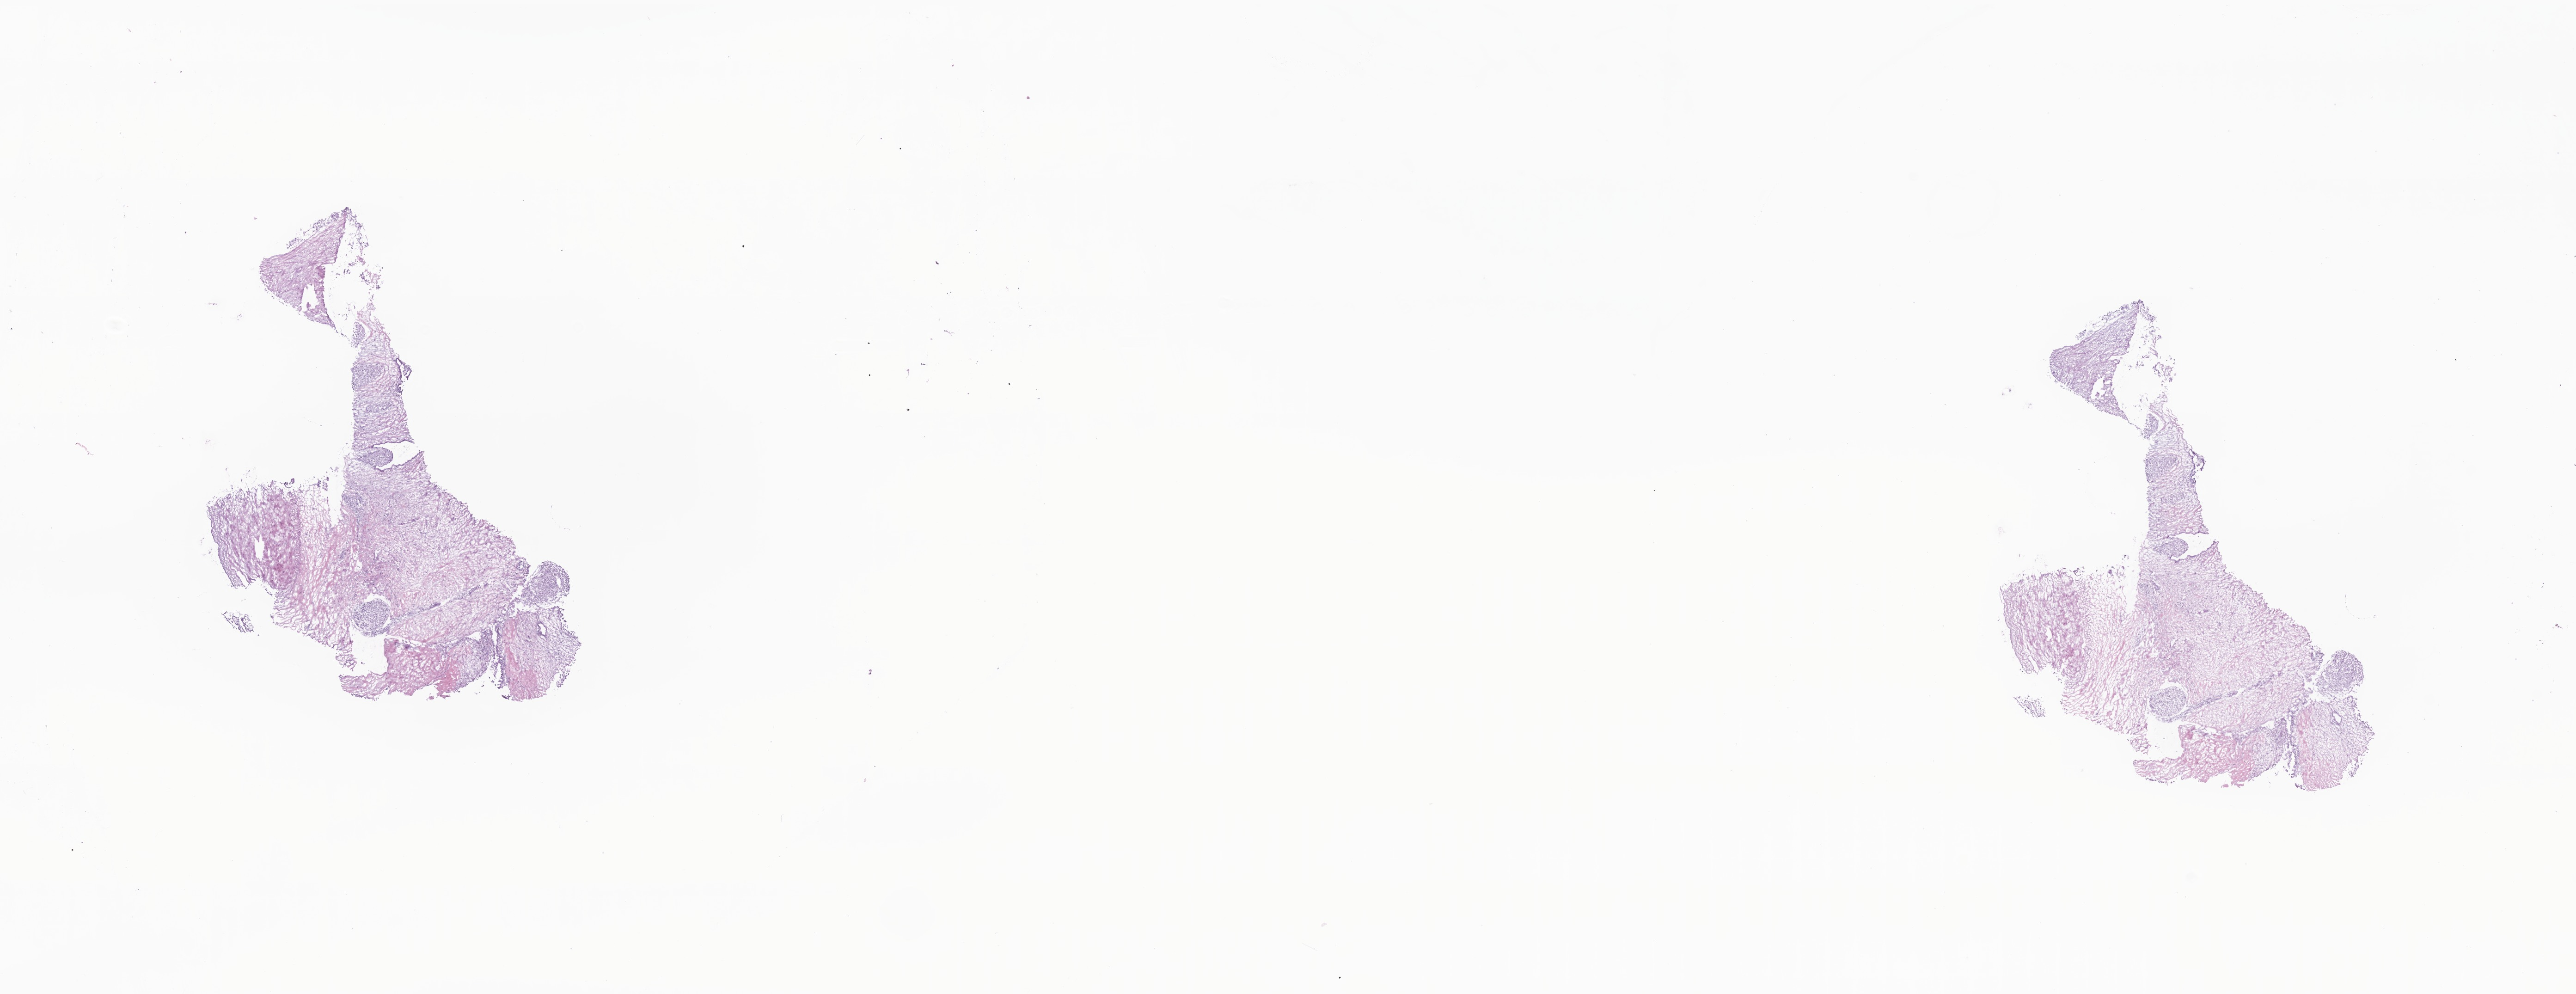
Whole-slide image, hematoxylin and eosin (H&E) stain — a low-resolution overview of the entire scanned area, about 23.5 x 9.1 mm. Frozen section (tissue freezing medium). Primary tumor. Site: body of pancreas. Patient: male, age at initial diagnosis 74 years. Slide review estimates, as recorded: tumor cells 12%, tumor nuclei 65%, stromal cells 87%, necrosis 1%, normal cells 0%. Infiltration values recorded for this section: lymphocyte infiltration 7%, monocyte infiltration 0%, neutrophil infiltration 0%.
Diagnosis: Infiltrating duct carcinoma, NOS.